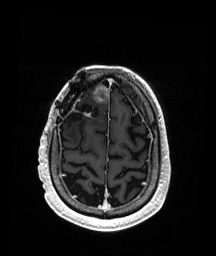
Brain MRI from a brain-tumour surgery series, one axial slice. Slice 44 of 192 in the series (ordered by position). T1-weighted post-contrast. 216 × 256 image matrix. Case-level facts recorded for this patient, not image findings: histopathology: Astrocytoma; WHO grade: 3; IDH mutation: yes; tumour location: Right Frontal.
Structures marked on this image (expert manual segmentation):
- previous resection cavity: bounding box (x1, y1, x2, y2) in pixels: (68, 104, 99, 124)
- tumour: (93, 85, 109, 103)